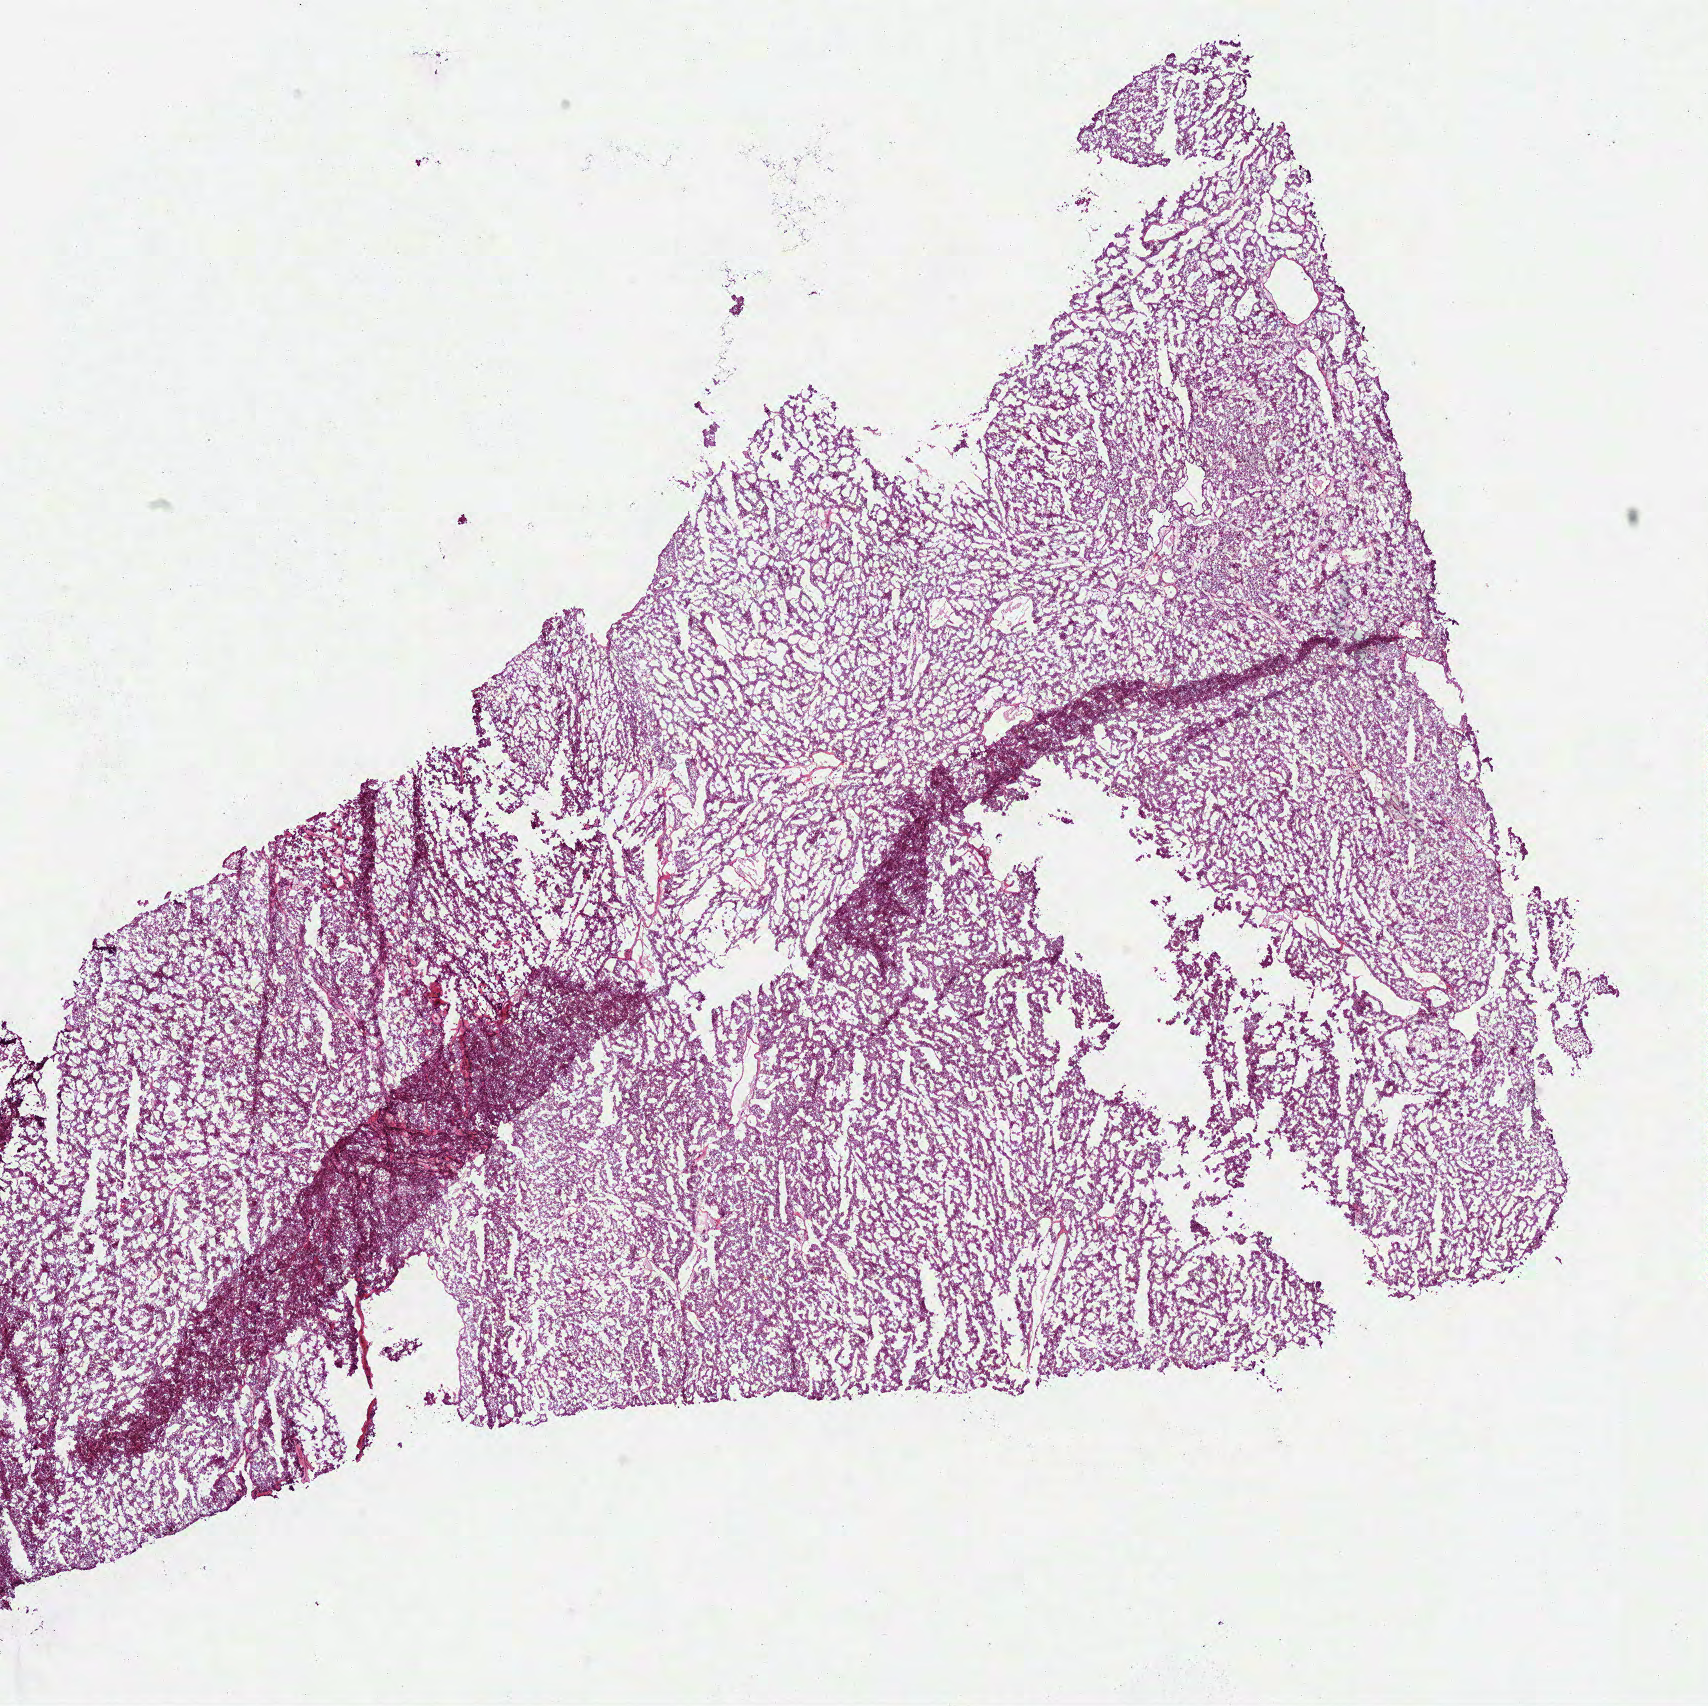
Whole-slide histology image, H&E, low-resolution overview of the scanned area, about 13.8 x 13.8 mm (slide scanned at 40x). Frozen section. Kidney, primary tumour sample. Female, age 86 years at initial diagnosis. Pathologist review of this section (percent, as recorded): tumour cells 100%, tumour nuclei 95%.
Histologic diagnosis: Renal cell carcinoma, chromophobe type.